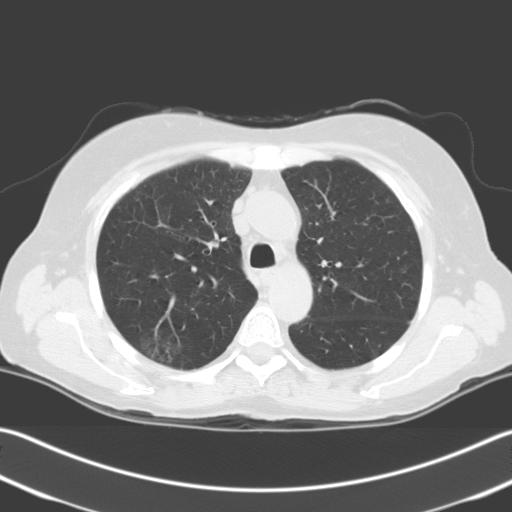
Low-dose screening chest CT, axial slice; first (baseline) screen; lung window (W 1500 / L -600 HU); 3.2 mm slice thickness; standard (soft-tissue) reconstruction kernel (C); slice 51 of 204 in the series; 512 × 512 image matrix. Female, age 67 years at enrolment. Current smoker at enrolment.
Expert-annotated lung lesion, bounding box [x1, y1, x2, y2] px = [125, 324, 186, 373]. The screening reader recorded 2 non-calcified nodules or masses ≥4 mm on this exam (right upper lobe, right upper lobe); which of them this box marks is not recorded. Participant outcome: lung cancer diagnosed 24 days after this screen — squamous cell carcinoma, NOS, right upper lobe, stage IIIA (AJCC 6th edition), 56 mm at pathology.